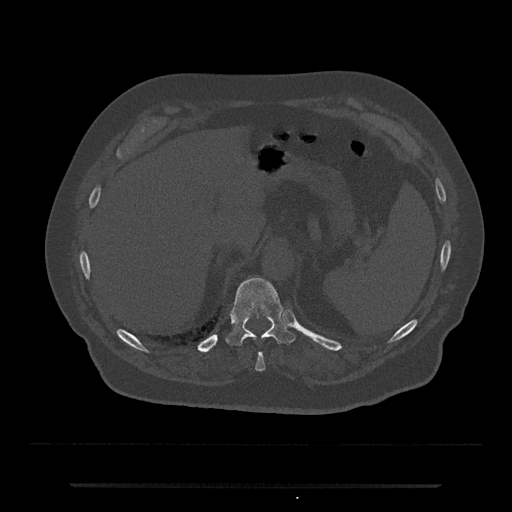
CT including the spine, one axial slice. Position 661 of 797 along the scan axis. Reconstruction kernel Br40s/3. 120 kVp. Bone window (W 1800 / L 400 HU). 512 × 512 image matrix, field of view 434 × 434 mm. Patient: male, 80 years. From the clinical record (not read from this slice): primary cancer: prostate; vertebrae with lytic lesions (as recorded): L1, T11.
Annotated regions visible in this slice (semi-automatically segmented with operator editing):
- T10 vertebra: bounding box (x1, y1, x2, y2) in pixels: (255, 353, 265, 371)
- T11 vertebra: (226, 277, 295, 346)